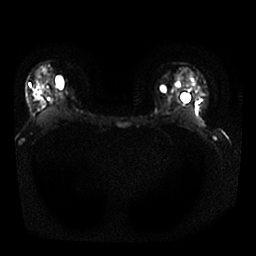
Breast MRI, one axial slice; position 19 of 25 along the scan axis; diffusion-weighted series; image 2 of 4 stored at this slice position (different b-values; order by instance number); 1.5 T; 4 mm slice thickness; 256 × 256 image matrix. Female patient.
Outlined on this slice (outlined manually by an expert reader):
- tumour on diffusion-weighted imaging: bounding box [x1, y1, x2, y2] px = [35, 66, 47, 94]